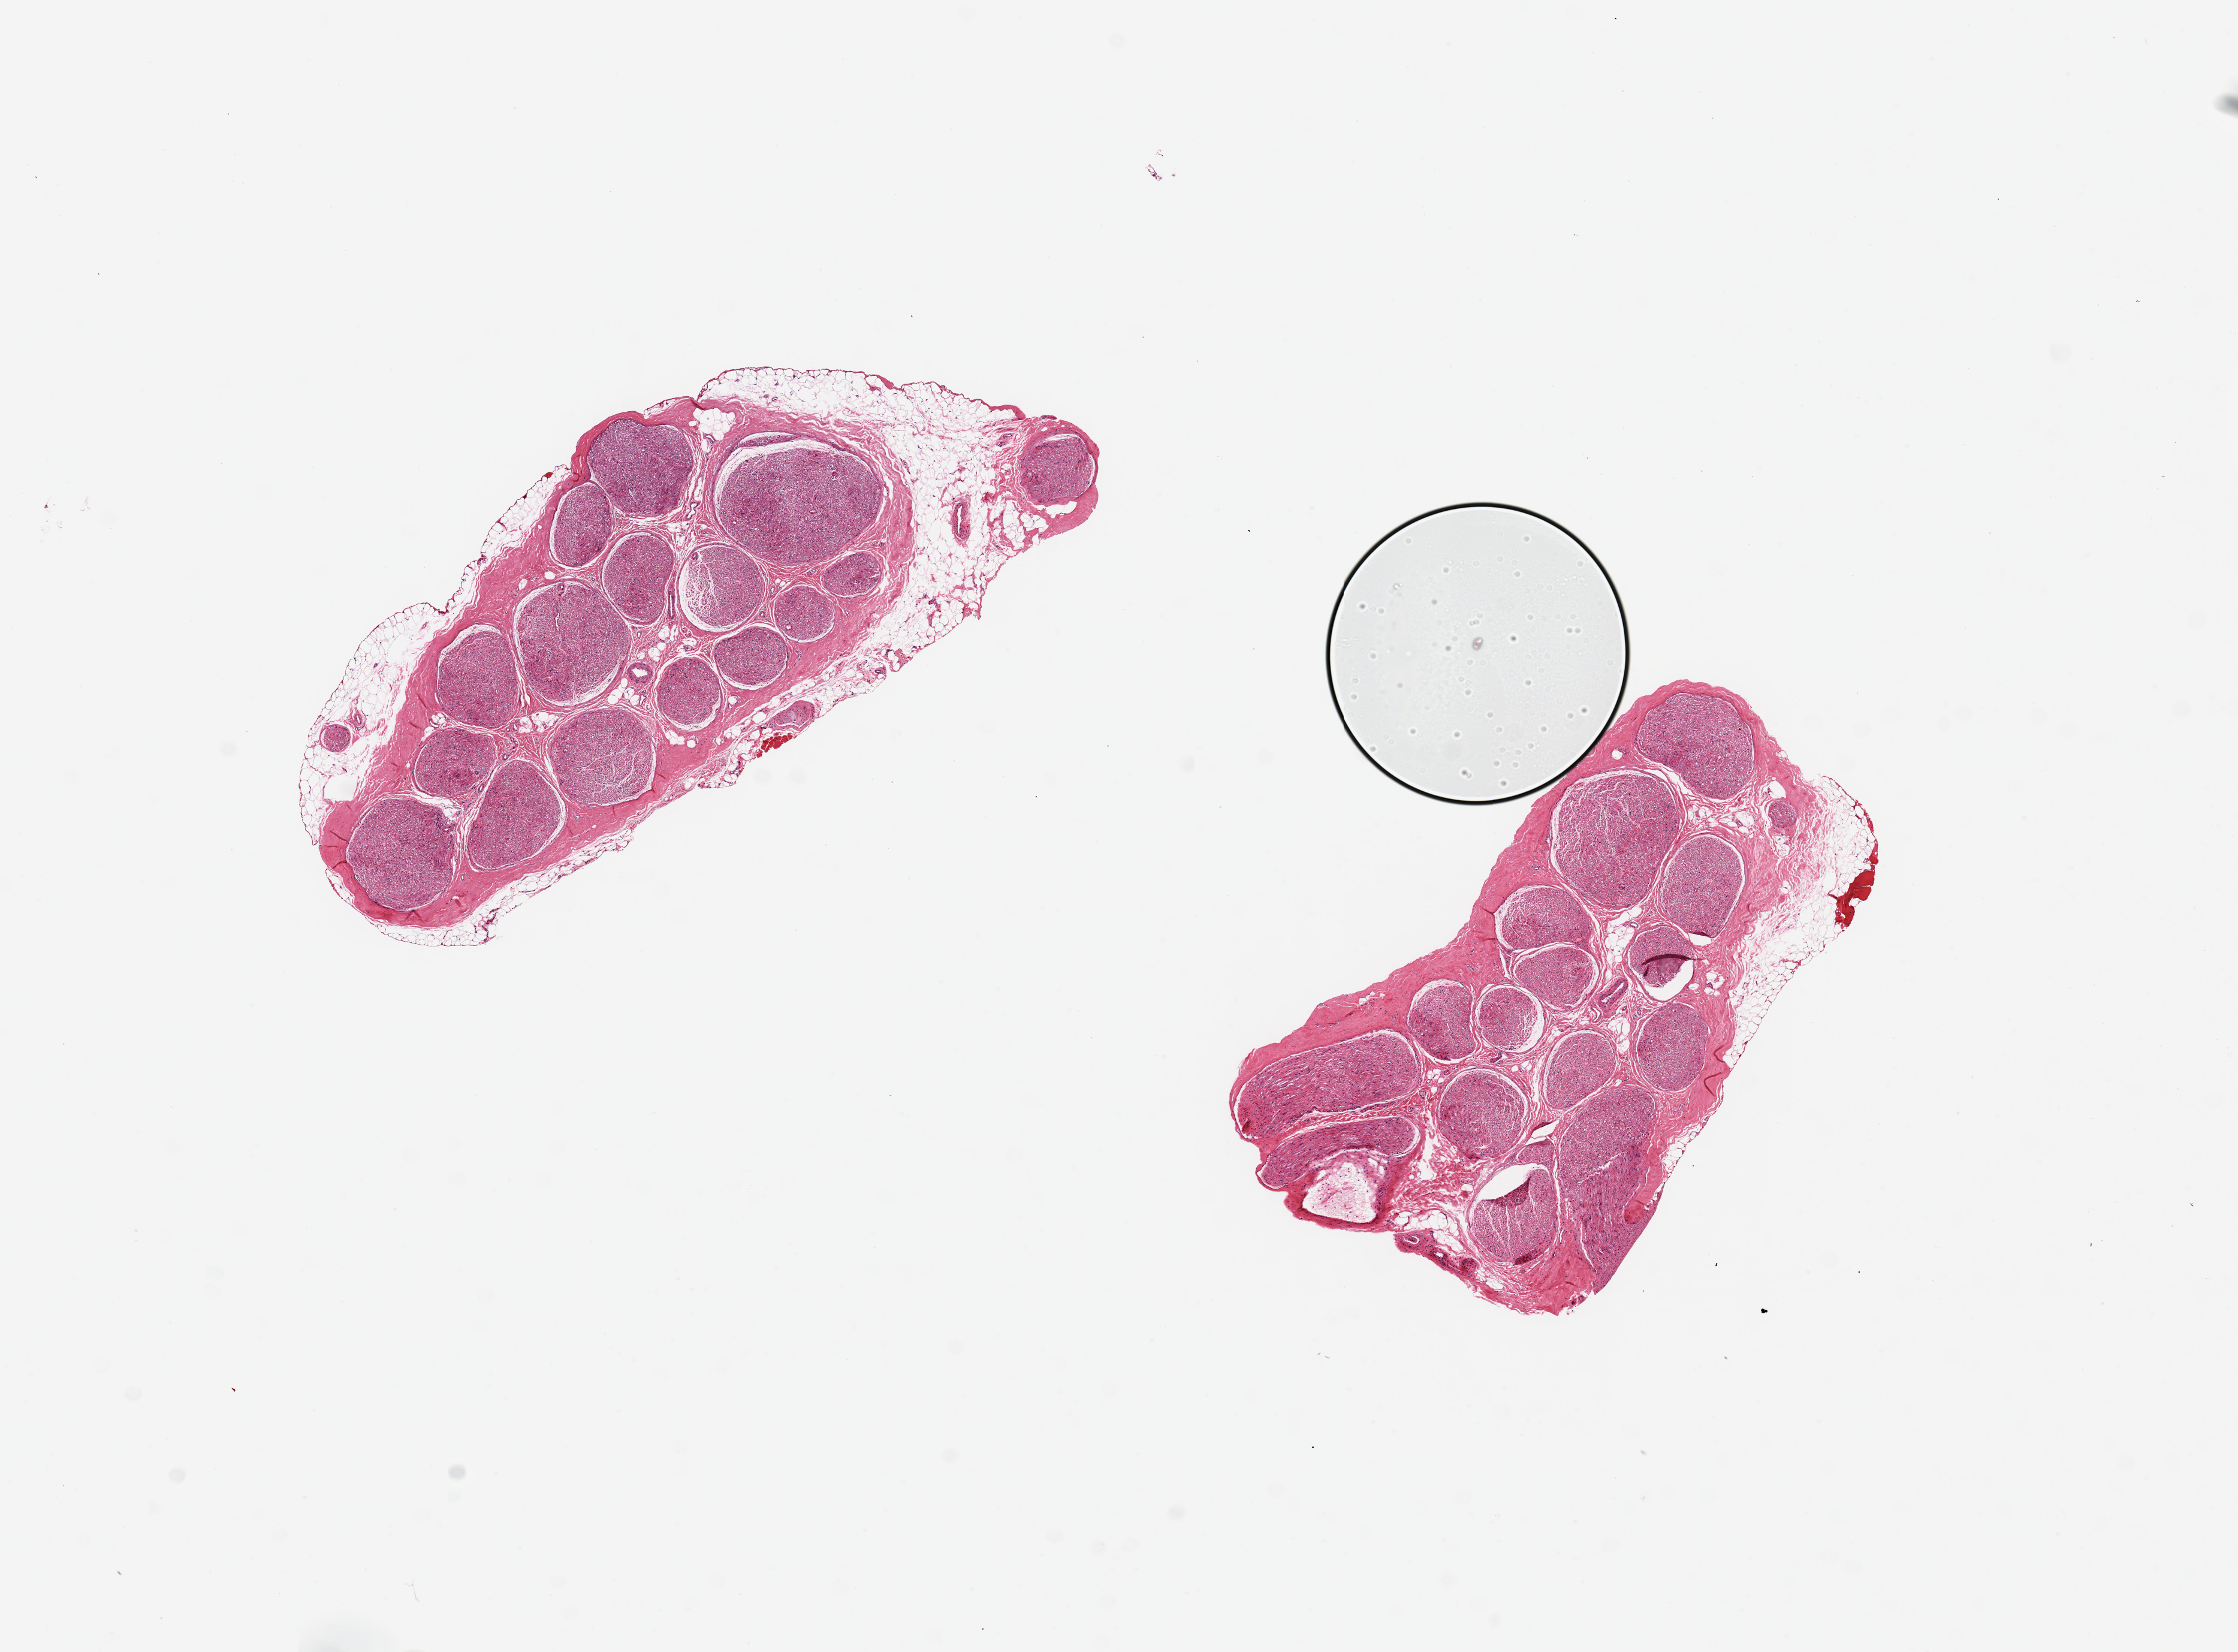
H&E whole-slide image — shown as a low-resolution overview of the whole scanned area (about 14.8 x 10.9 mm); PAXgene-fixed paraffin-embedded (PFPE) section; section of tibial nerve (target tissue); tissue donor sample. Donor sex: male.
- pathologist's review note for this sample: 2 pieces ~3.5mm d; ~ 0.5mm discontinuous fat layer